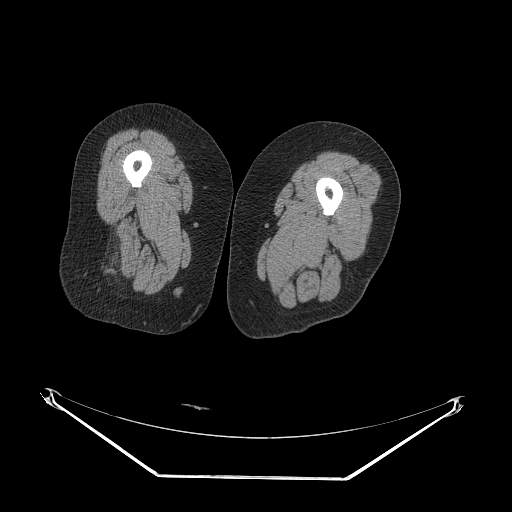
CT of an extremity soft-tissue mass (from a PET/CT study), one axial slice; 140 kVp; soft-tissue window (W 400 / L 40 HU); 3.75 mm slice thickness; 512 × 512 image matrix, field of view 500 × 500 mm. Female patient. From the clinical record (not read from this slice): histological type: synovial sarcoma; grade: intermediate; site of the primary tumour: right buttock.
Structures marked on this image (expert contour drawn on MRI and transferred to this co-registered scan by the dataset authors):
- gross tumour volume including surrounding oedema: box from (x=94, y=238) to (x=113, y=277) px